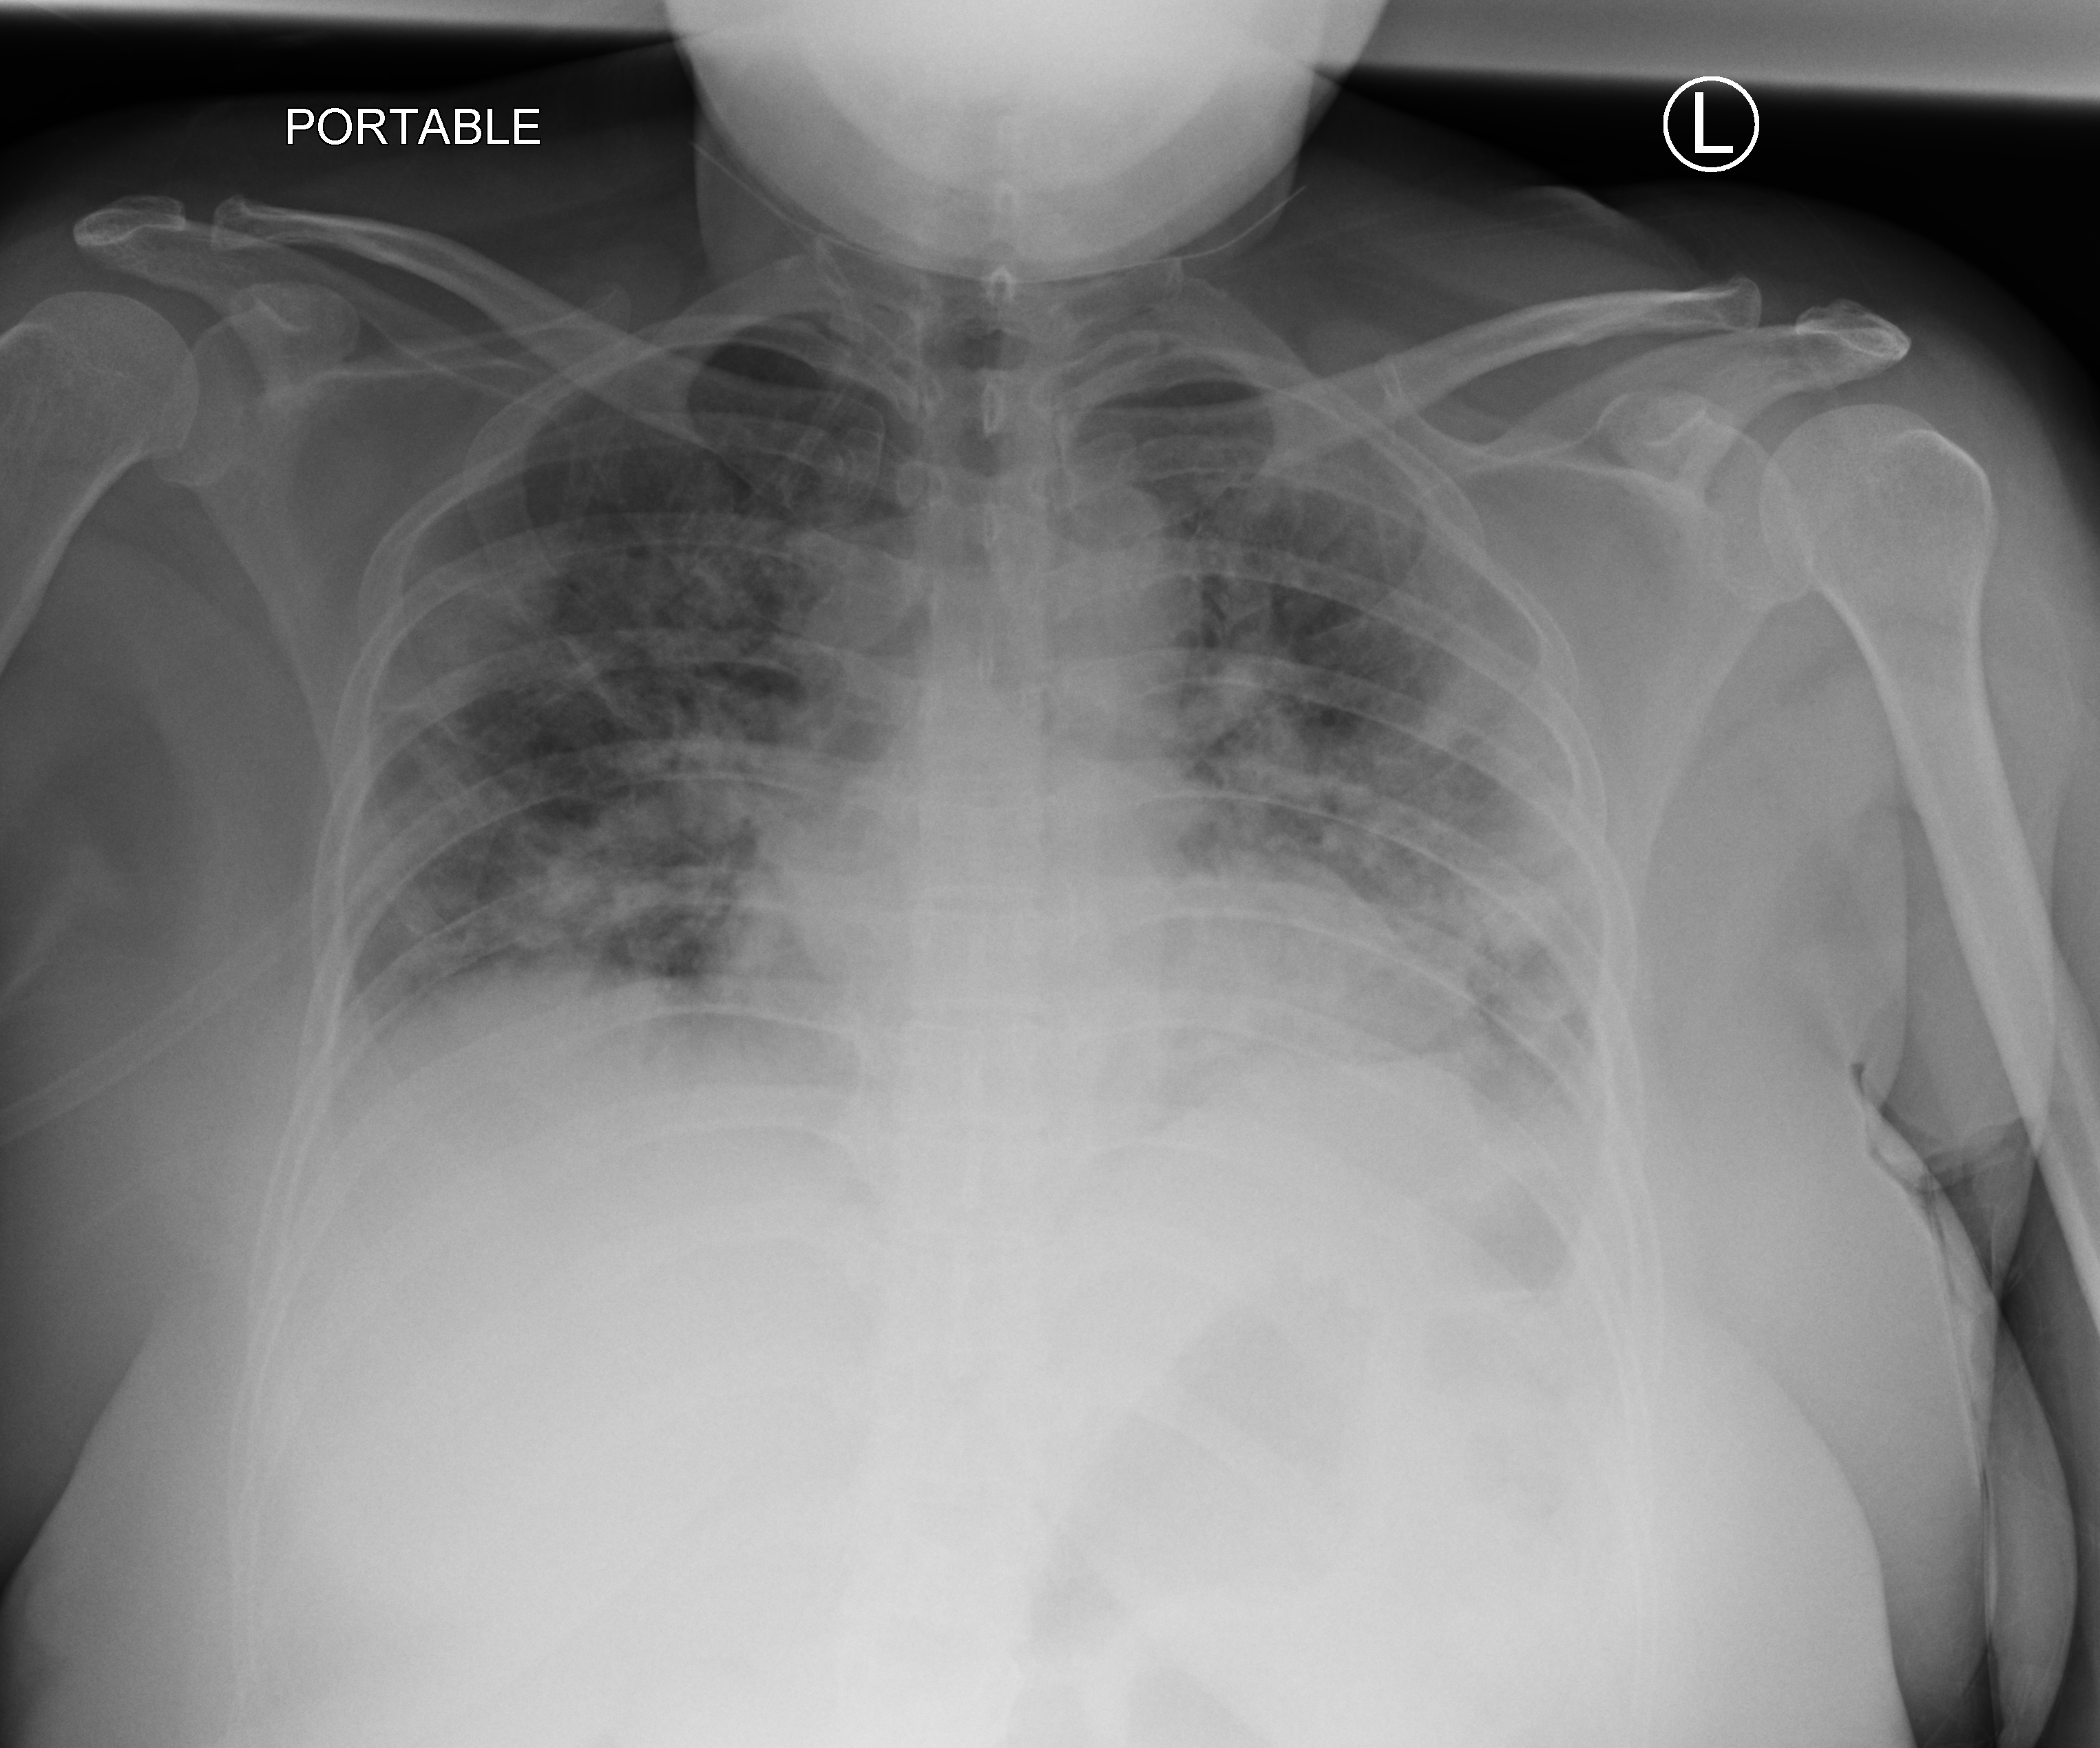
Chest X-ray (portable); anteroposterior (AP) projection. Patient hospitalised with COVID-19; female, aged 18–59 years.
Admission-level facts for this patient (not findings on this image; timing relative to this image not recorded):
- mechanically ventilated during this hospital stay: yes
- admitted to intensive care during this hospital stay: yes
- diabetes (admission record): no